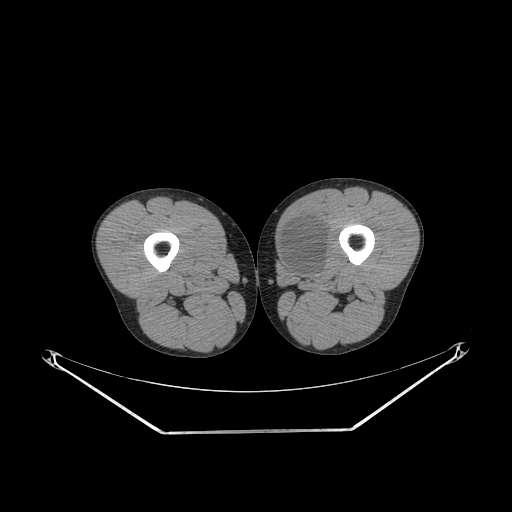
CT of an extremity soft-tissue mass (from a PET/CT study), one axial slice; slice 242 of 311 in the series (ordered by position); reconstruction kernel SOFT; soft-tissue window (W 400 / L 40 HU); 3.75 mm slice thickness; 512 × 512 image matrix, field of view 500 × 500 mm. Male patient. Case-level facts recorded for this patient, not image findings: histological type: mixoid liposarcoma; grade: low; site of the primary tumour: left thigh.
Annotated regions visible in this slice (expert contour drawn on MRI and transferred to this co-registered scan by the dataset authors):
- gross tumour volume (mass): bounding box <279,217,328,277> (left, top, right, bottom; pixels)